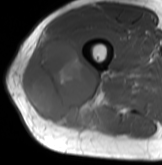
MRI of an extremity soft-tissue mass, one axial slice. Position 43 of 61 along the scan axis. MR volume resampled by the dataset authors to the PET/CT grid (not the native acquisition matrix). 3.27 mm slice thickness. 162 × 165 image matrix, field of view 158 × 161 mm. Male patient. Case-level facts recorded for this patient, not image findings: histological type: poorly differentiated synovial sarcoma; grade: high; site of the primary tumour: right buttock.
Annotated regions visible in this slice (expert contour drawn on MRI and transferred to this co-registered scan by the dataset authors):
- gross tumour volume including surrounding oedema: bounding box <22,31,104,128> (left, top, right, bottom; pixels)
- gross tumour volume (mass): <22,33,101,128>